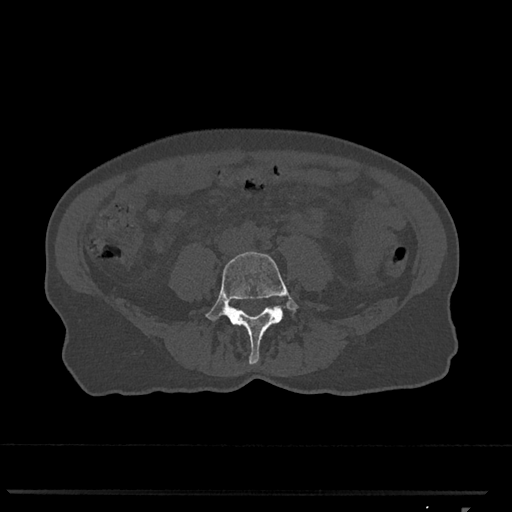
CT including the spine, one axial slice. Slice 207 of 793 in the series (ordered by position). Reconstruction kernel Br40s/3. 120 kVp. Bone window (W 1800 / L 400 HU). 0.5 mm slice thickness. 512 × 512 image matrix, field of view 380 × 380 mm. Female patient, age 62 years. Case-level facts recorded for this patient, not image findings: primary cancer: renal.
Annotated regions visible in this slice (semi-automatically segmented with operator editing):
- L4 vertebra: bounding box (x1, y1, x2, y2) in pixels: (205, 251, 299, 365)